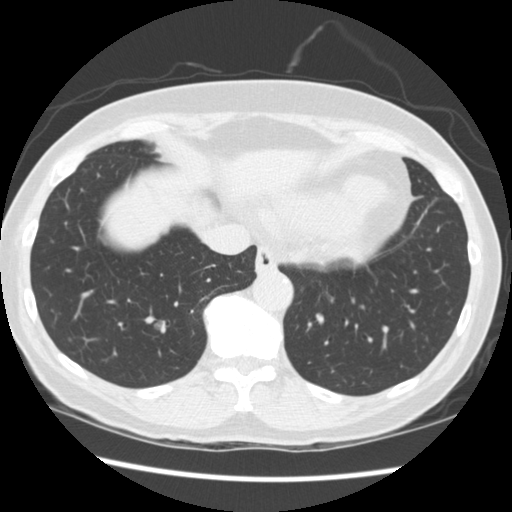
Low-dose screening chest CT, one axial slice; position 71 of 262 along the scan axis; reconstruction kernel STANDARD; 120 kVp; lung window (W 1500 / L -600 HU); 512 × 512 image matrix, field of view 340 × 340 mm.
Outlined on this slice (outlined manually by an expert reader):
- lesion 1 (tumor, lower lobe of right lung): bounding box [x1, y1, x2, y2] px = [161, 321, 165, 333]